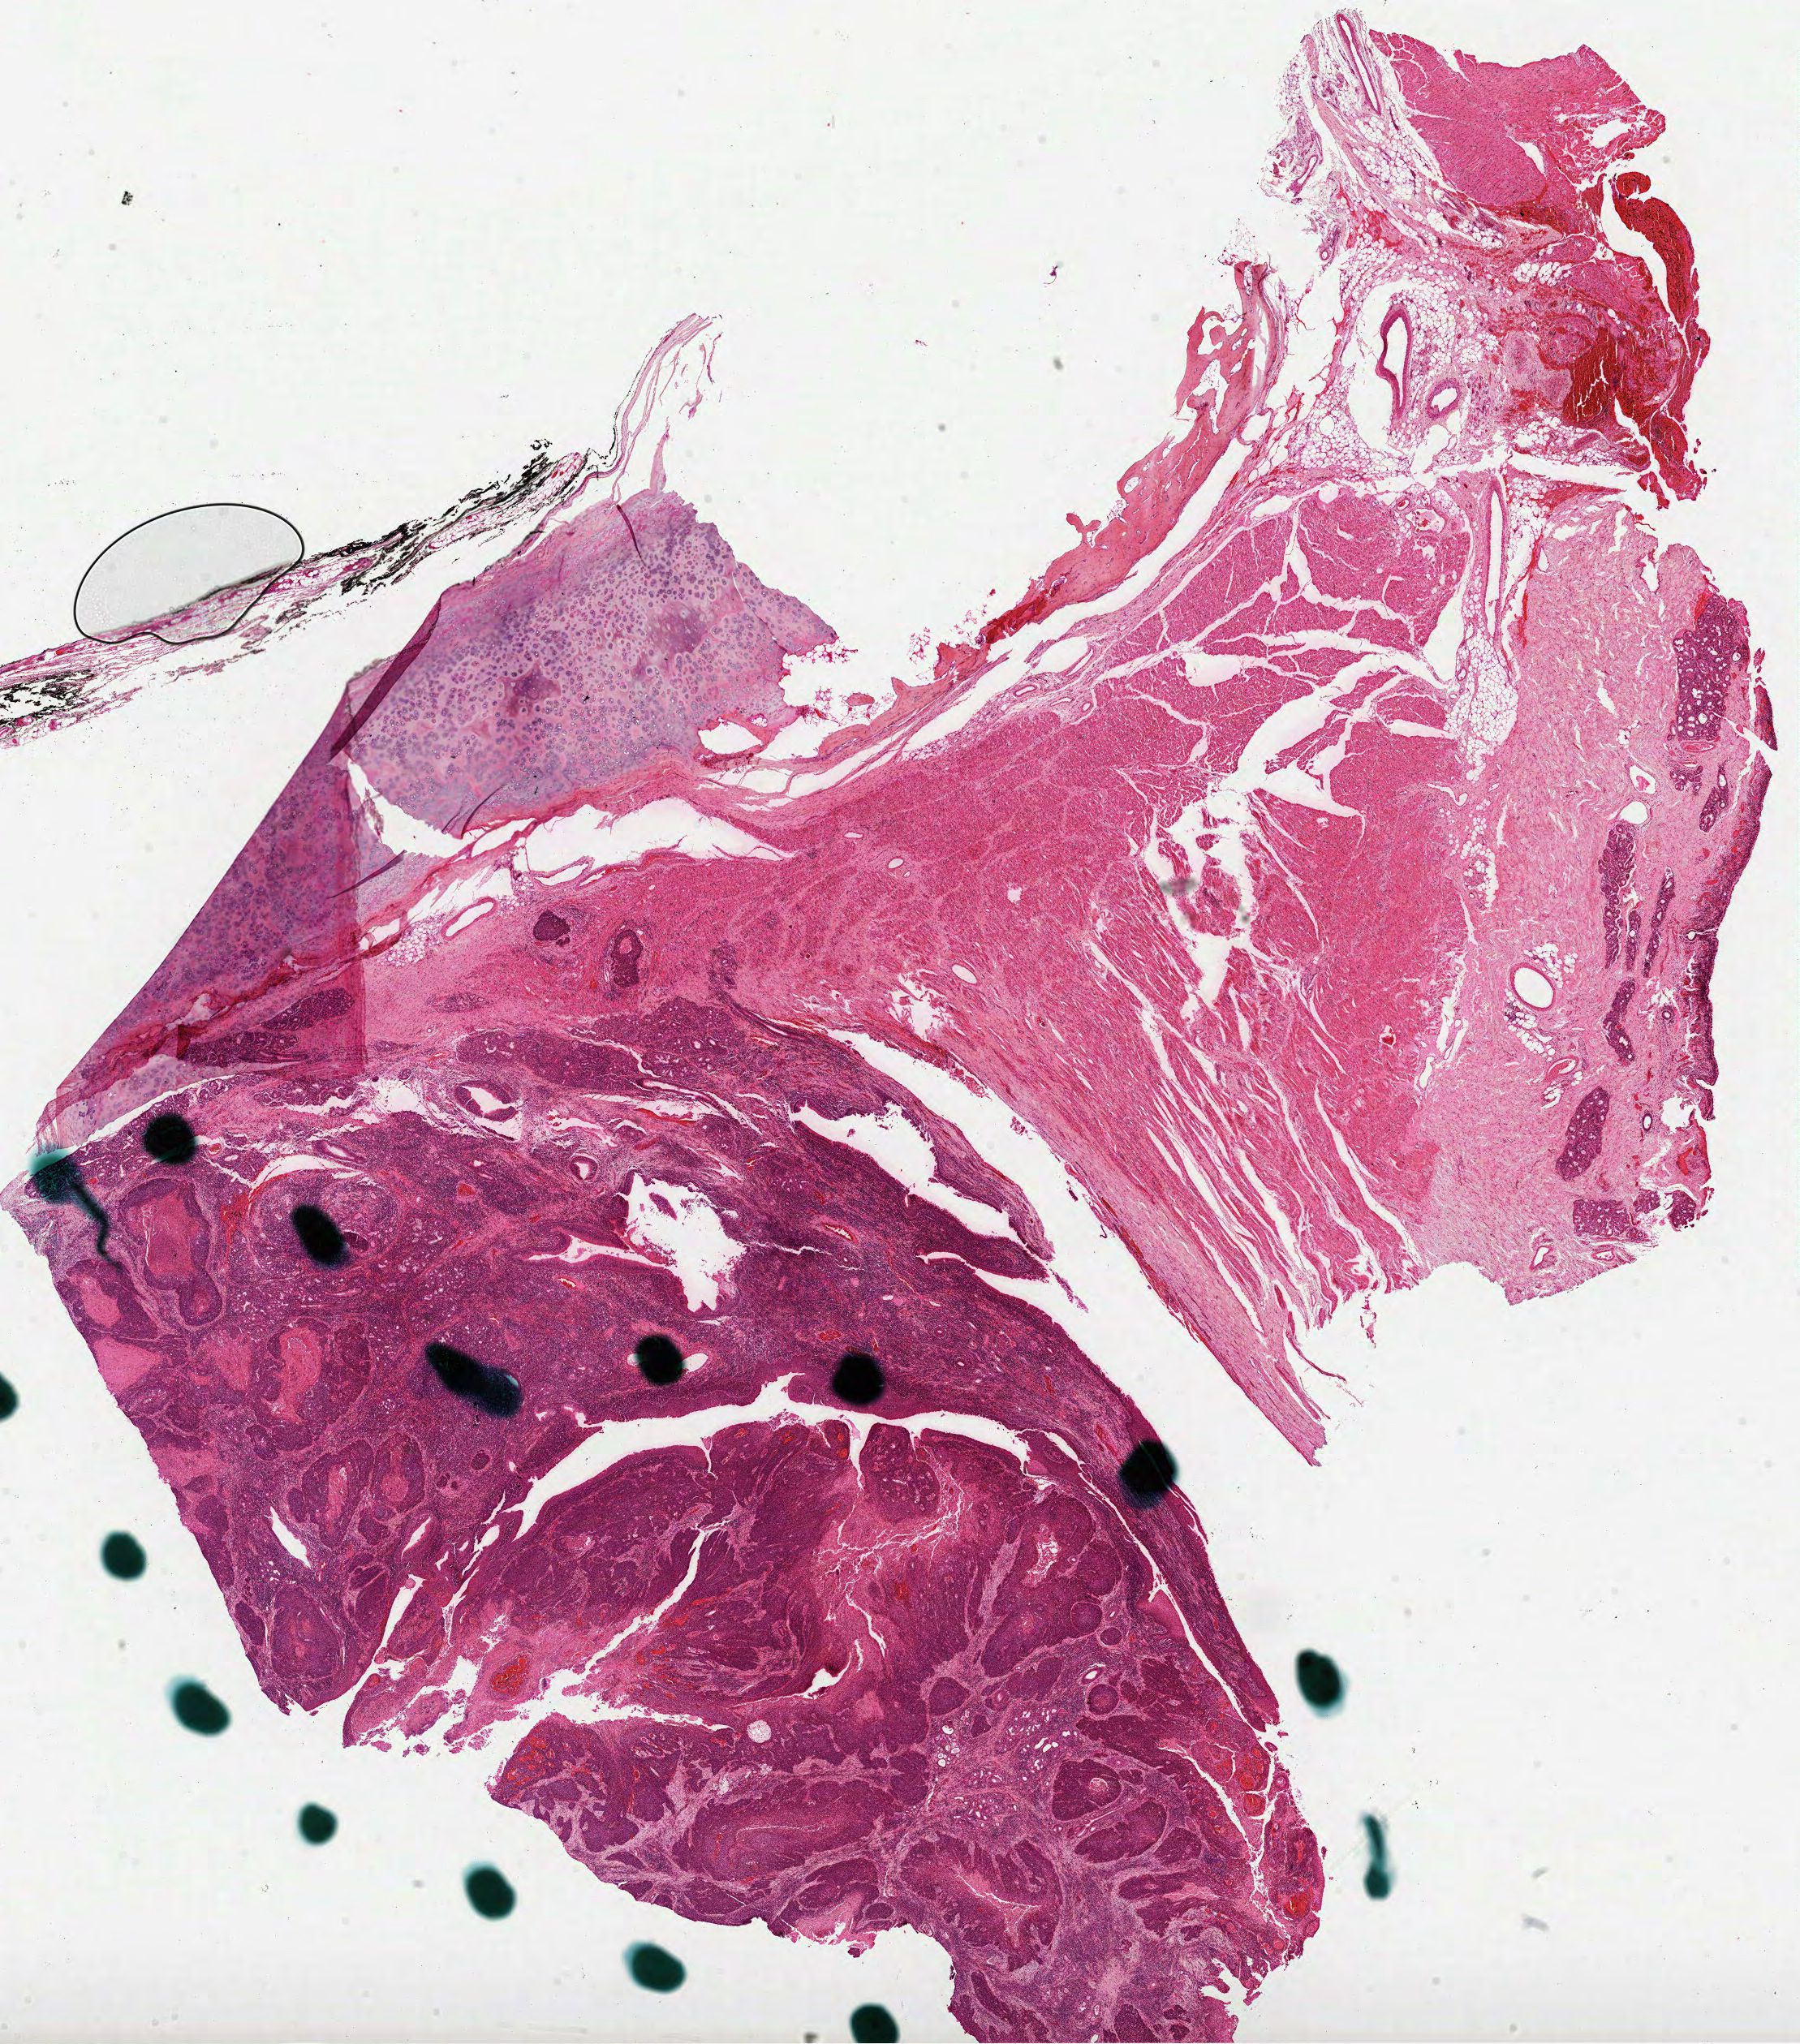
Hematoxylin and eosin (H&E) stained whole-slide image, whole scanned area (about 17.9 x 20.3 mm, acquisition: 40x scan) shown as a low-resolution overview, formalin-fixed paraffin-embedded (FFPE) diagnostic section, sample: primary tumour, head and neck. Male, age 61 years at initial diagnosis. Histologic grade: G2 (moderately differentiated).
Lymph nodes positive (case pathology): 3 of 54 examined. AJCC pathologic stage: IVA (7th edition). Histologic diagnosis: Squamous cell carcinoma, NOS (larynx, NOS).